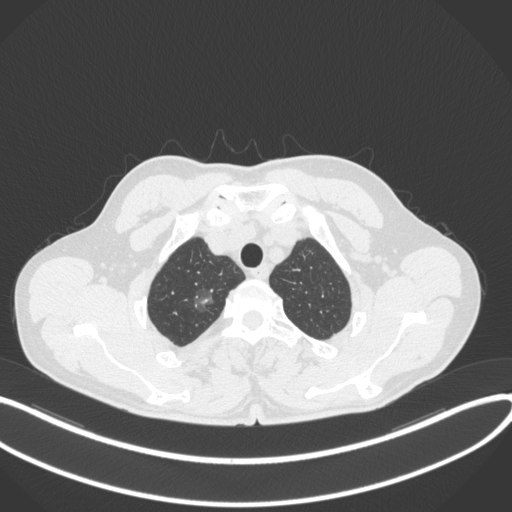
Chest CT, one axial slice. Slice 334 of 407 in the series (ordered by position). 120 kVp. Lung window (W 1500 / L -600 HU). 512 × 512 image matrix, field of view 400 × 400 mm. Male patient, age 58 years. Case-level facts recorded for this patient, not image findings: clinical TNM (as recorded): T1c N0 M0; histopathological grade: G1-2.
Structures marked on this image (bounding box drawn by a radiologist):
- lung tumour (recorded histology: adenocarcinoma): bounding box <192,288,214,311> (left, top, right, bottom; pixels)